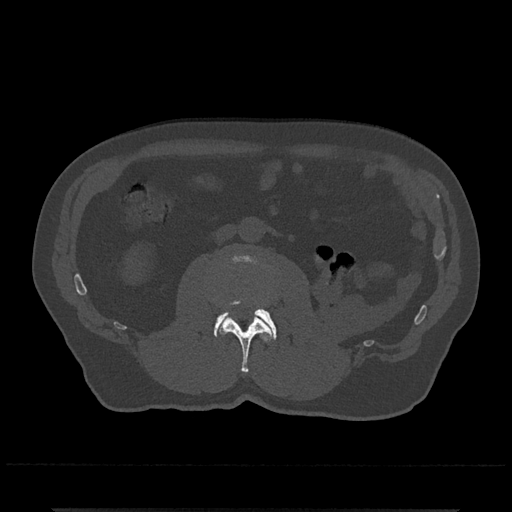
CT including the spine, one axial slice; position 265 of 797 along the scan axis; reconstruction kernel Br40s/3; bone window (W 1800 / L 400 HU); 0.5 mm slice thickness; 512 × 512 image matrix, field of view 393 × 393 mm. Patient: male, 67 years. From the clinical record (not read from this slice): primary cancer: prostate.
Annotated regions visible in this slice (semi-automatically segmented with operator editing):
- L2 vertebra: bounding box [x1, y1, x2, y2] px = [220, 300, 272, 373]
- L3 vertebra: [214, 254, 277, 340]